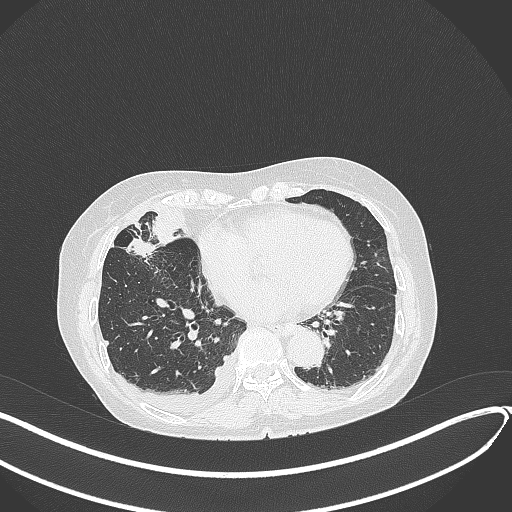
Chest CT, one axial slice. Slice 144 of 418 in the series (ordered by position). Reconstruction kernel B70f. 120 kVp. Lung window (W 1500 / L -600 HU). 512 × 512 image matrix, field of view 400 × 400 mm. Female patient, age 75 years. Case-level facts recorded for this patient, not image findings: clinical TNM (as recorded): T2a N3 M0.
Outlined on this slice (bounding box drawn by a radiologist):
- lung tumour (recorded histology: adenocarcinoma): bounding box <127,236,158,257> (left, top, right, bottom; pixels)